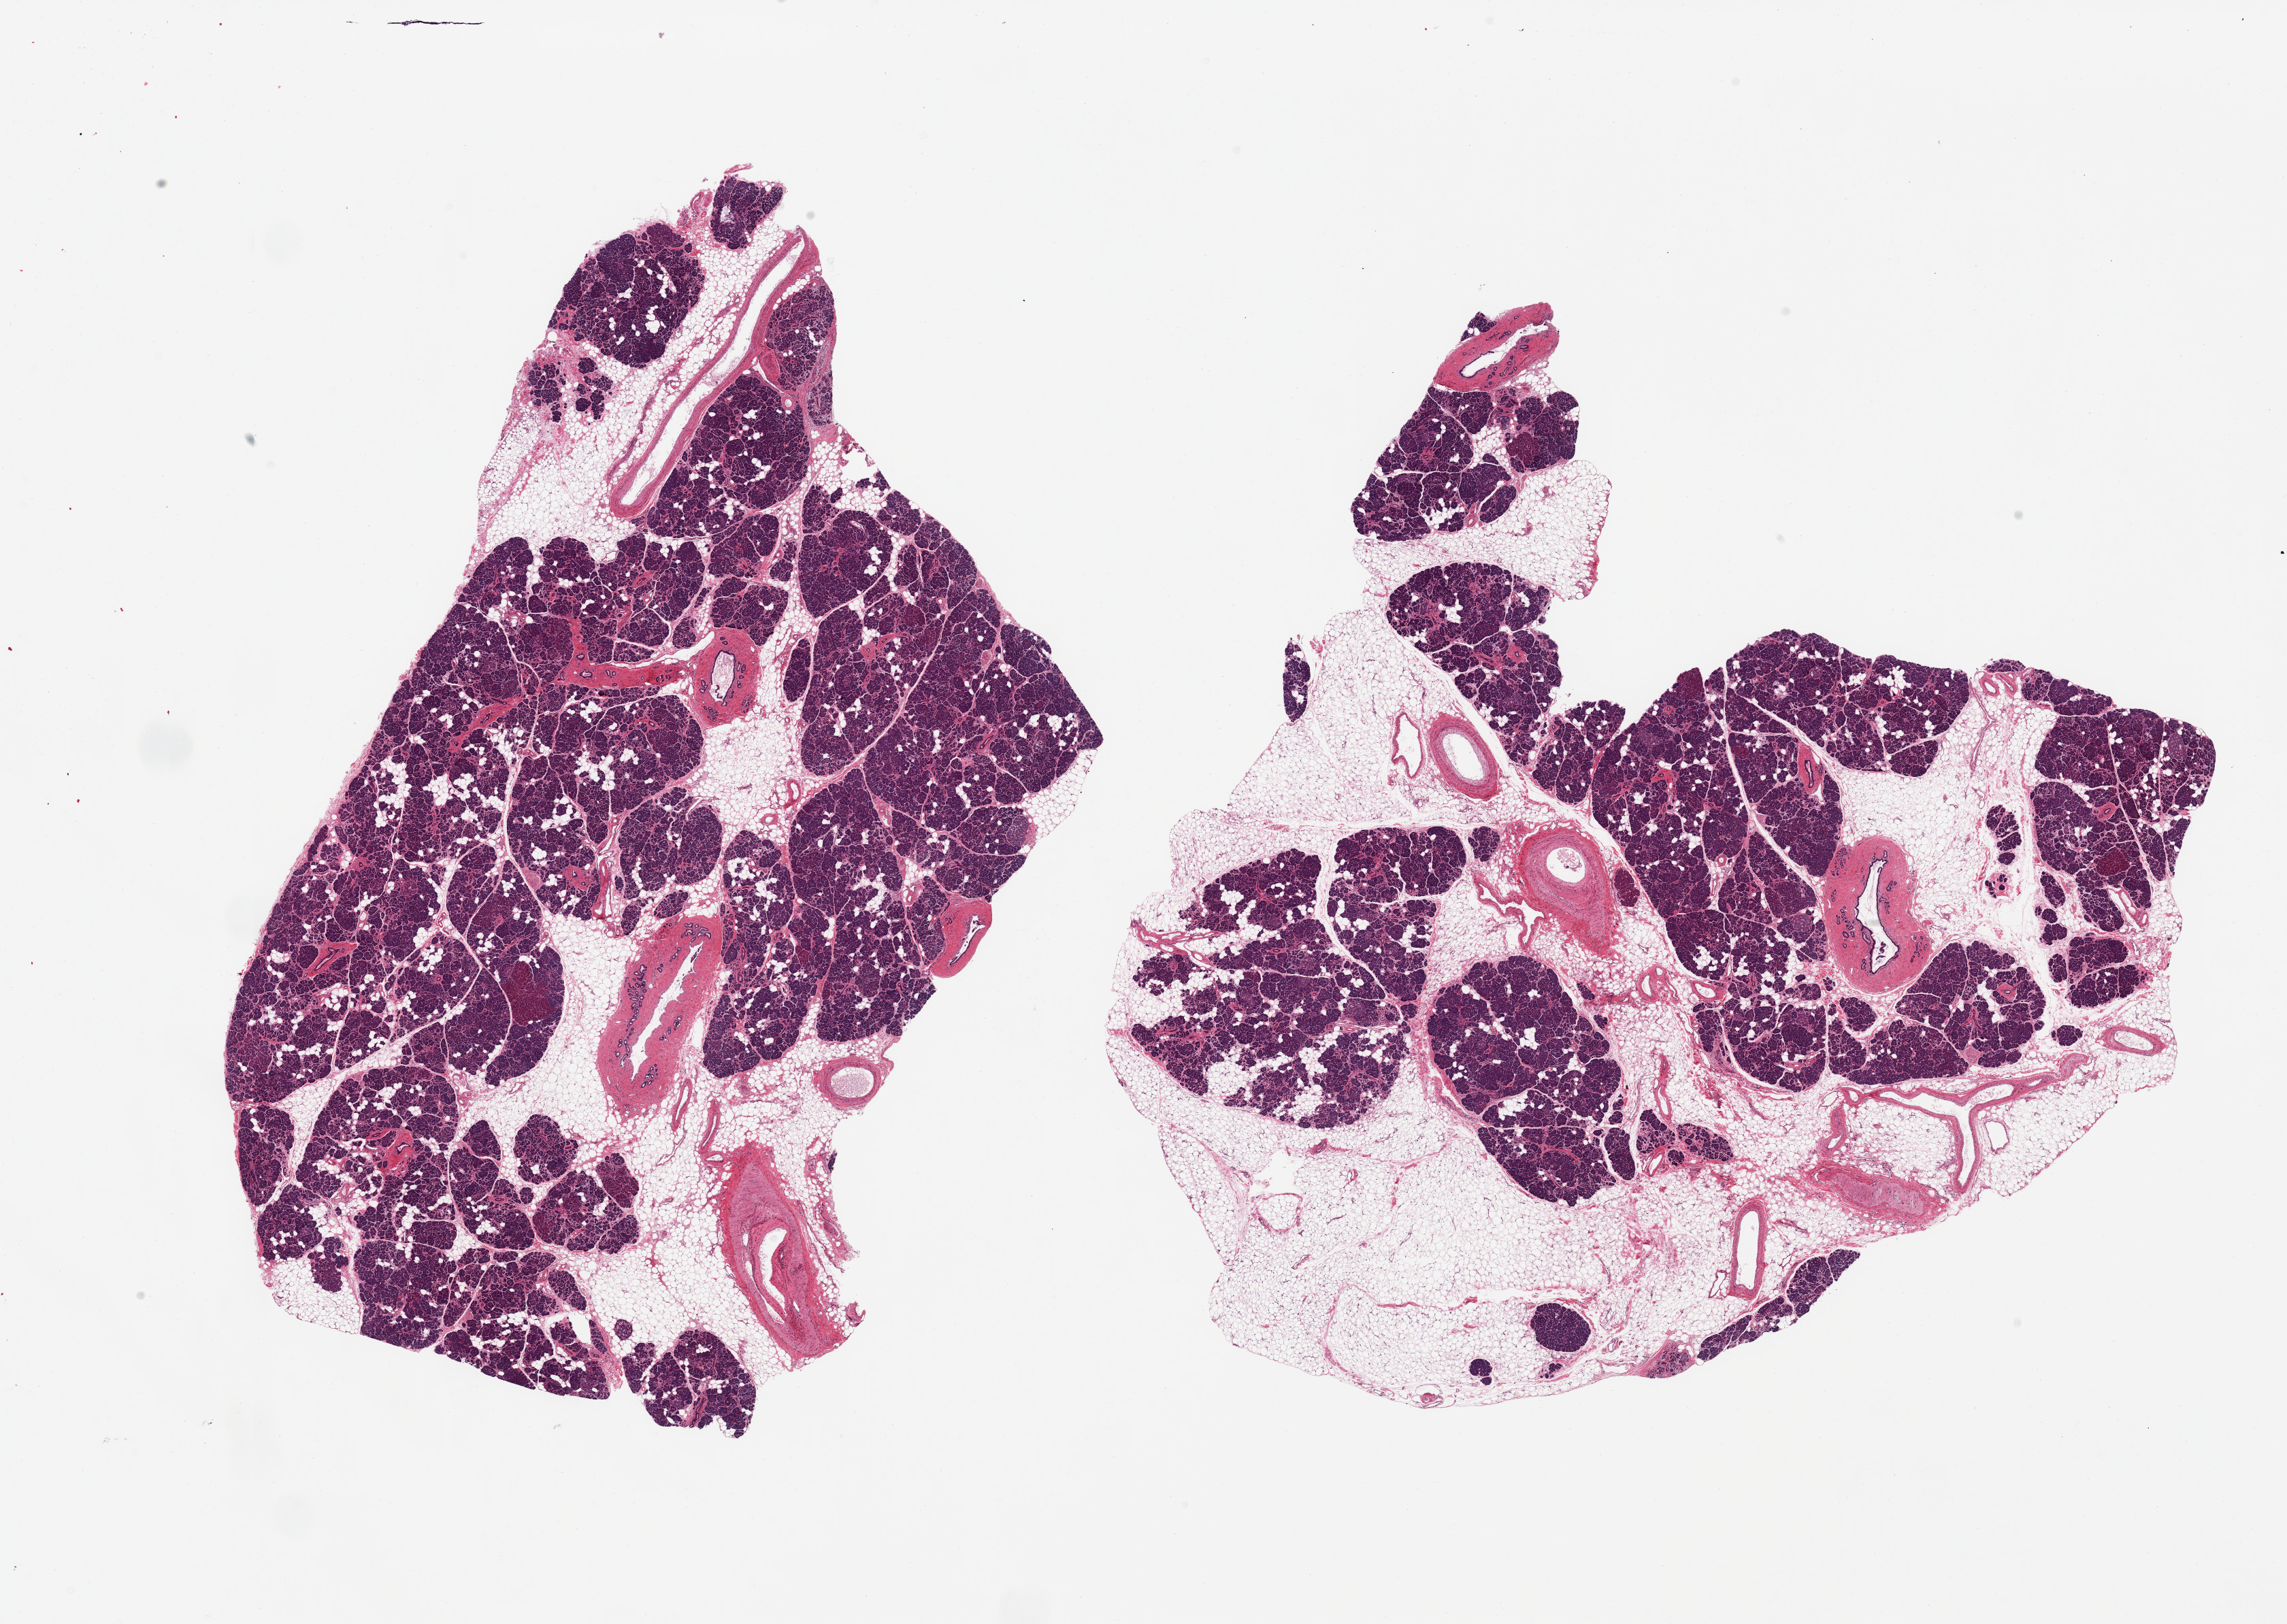
Whole-slide image, haematoxylin and eosin stain — whole scanned area (about 26.6 x 18.9 mm, from a 20x scan) shown as a low-resolution overview. PAXgene-fixed, paraffin-embedded tissue. Target tissue: pancreas. Tissue donor sample. Donor: male.
- review note (as recorded): 2 pieces ~30% fat; Islets rare but well preserved